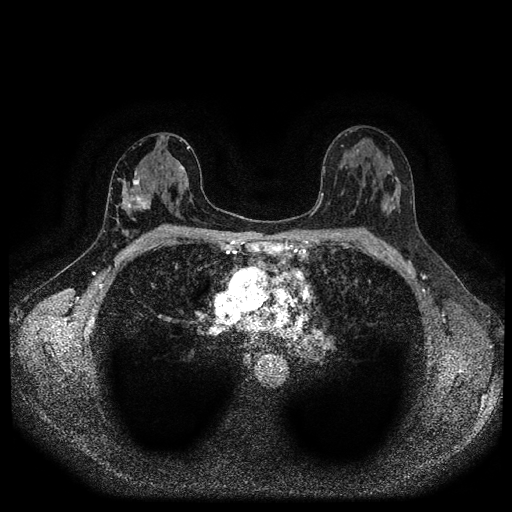
Breast MRI (dynamic contrast-enhanced, multi-phase), one axial slice. Position 57 of 116 along the scan axis. Dynamic contrast-enhanced series, time point 2 of 5 at this slice position (early post-contrast). 1.5 T. TE 2.7 ms, TR 5.4 ms. 2 mm slice thickness. 512 × 512 image matrix, field of view 330 × 330 mm. Female patient, age 42 years.
Structures marked on this image (semi-automatically segmented with operator editing):
- breast lesion (labelled 'tumour' in the annotation; benign lesions carry a separate 'benign' label): box from (x=124, y=175) to (x=151, y=214) px